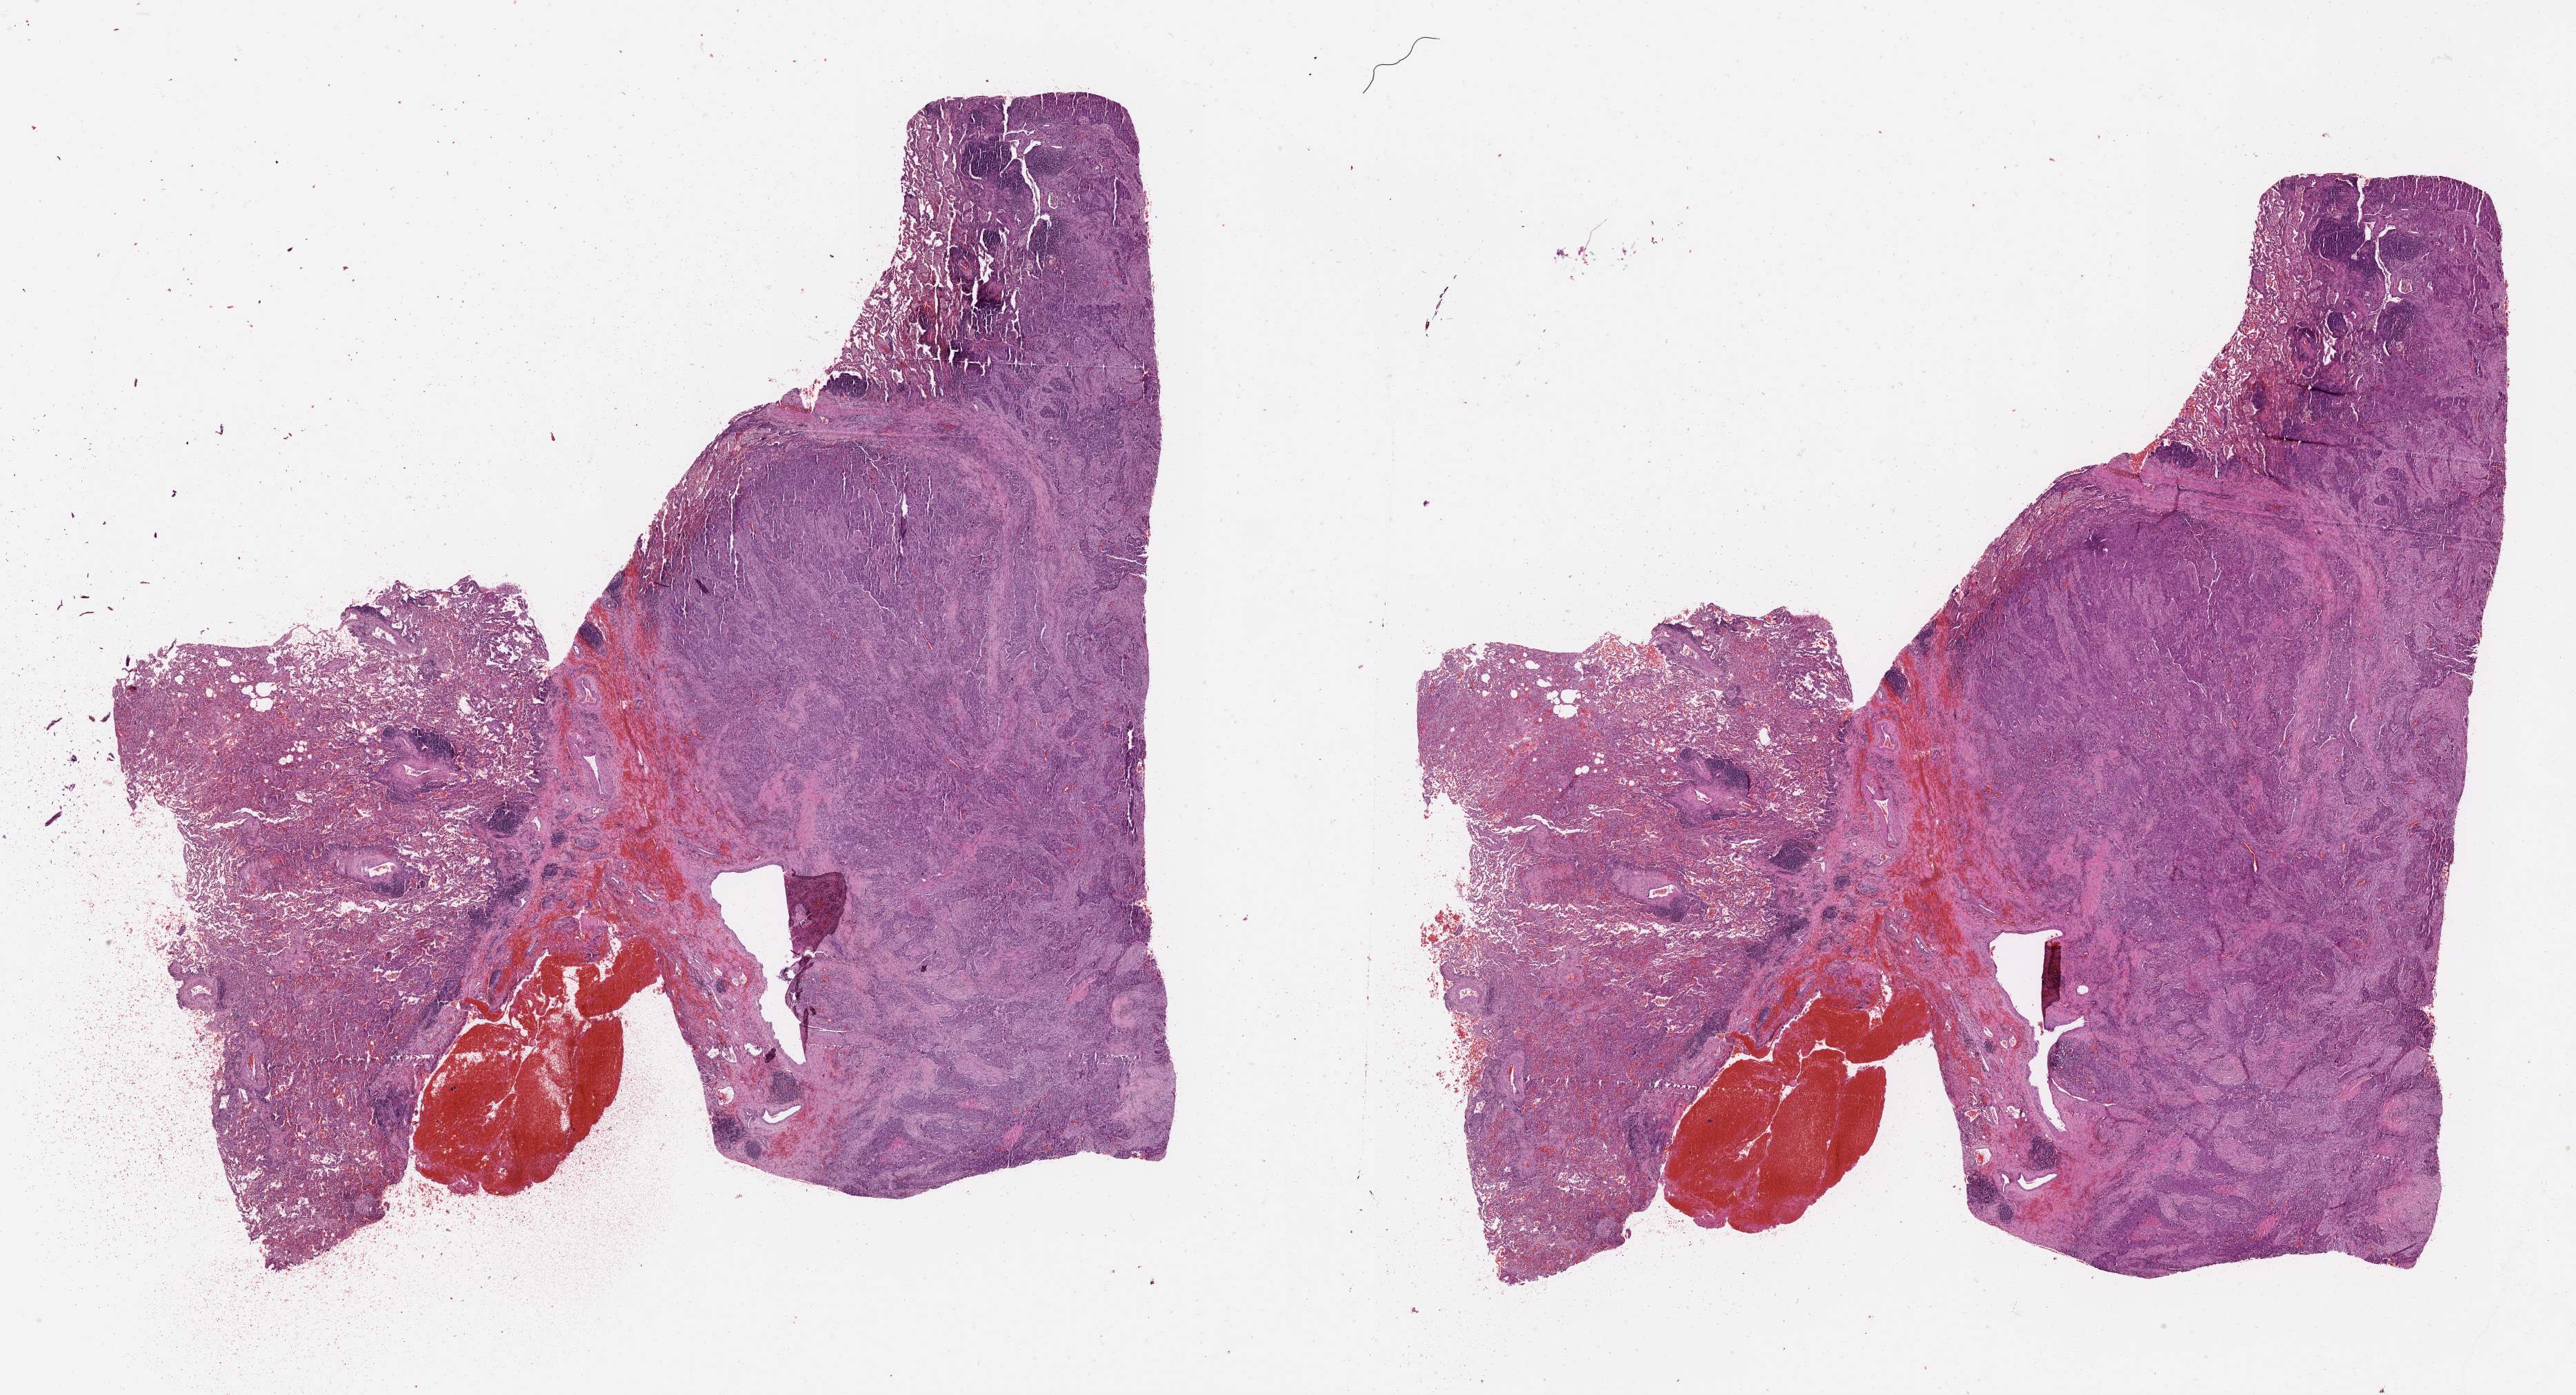
Digitized H&E tissue section (whole slide) — shown as a low-resolution overview of the whole scanned area (about 30.1 x 16.3 mm, from a 20x scan); lung, tumour tissue. 62-year-old female patient.
- patient diagnosis (cohort enrolment): squamous cell carcinoma (lung)